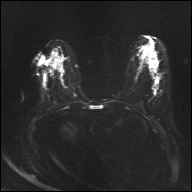
Breast MRI, one axial slice; position 17 of 32 along the scan axis; diffusion-weighted series; image 2 of 4 stored at this slice position (different b-values; order by instance number); 1.5 T; 192 × 192 image matrix. Female patient.
Structures marked on this image (expert manual segmentation):
- tumour on diffusion-weighted imaging: box from (x=155, y=87) to (x=157, y=89) px